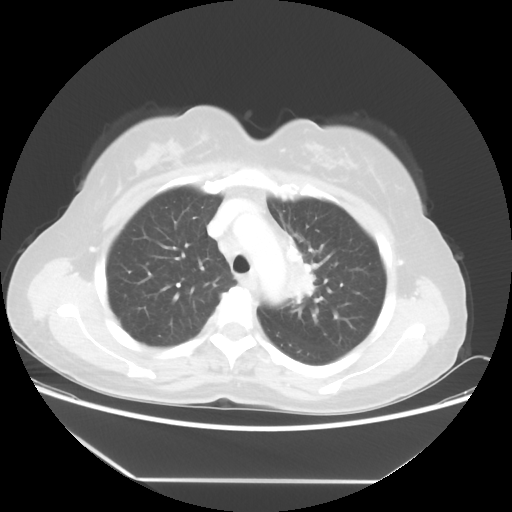
Chest CT, one axial slice. Position 39 of 52 along the scan axis. 100 kVp. Lung window (W 1500 / L -600 HU). 512 × 512 image matrix, field of view 390 × 390 mm. Patient: female, 50 years. From the clinical record (not read from this slice): clinical TNM (as recorded): T2 N3 M0.
Outlined on this slice (bounding box drawn by a radiologist):
- lung tumour (recorded histology: adenocarcinoma): bounding box (x1, y1, x2, y2) in pixels: (278, 242, 347, 321)